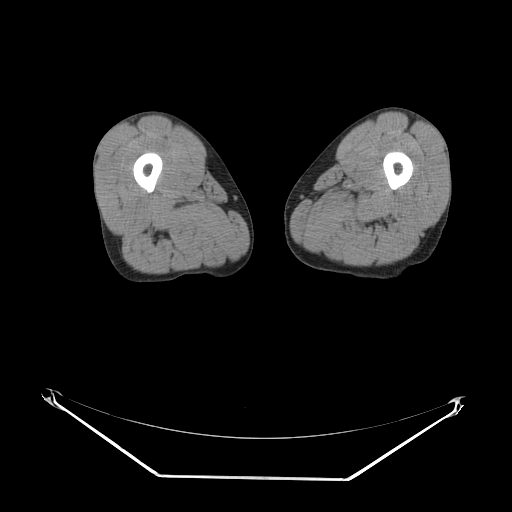
CT of an extremity soft-tissue mass (from a PET/CT study), one axial slice; slice 4 of 267 in the series (ordered by position); reconstruction kernel SOFT; soft-tissue window (W 400 / L 40 HU); 512 × 512 image matrix, field of view 500 × 500 mm. Male patient. Case-level facts recorded for this patient, not image findings: histological type: pleiomorphic liposarcoma; grade: high; site of the primary tumour: left thigh.
Annotated regions visible in this slice (expert contour drawn on MRI and transferred to this co-registered scan by the dataset authors):
- gross tumour volume including surrounding oedema: box from (x=343, y=212) to (x=360, y=222) px